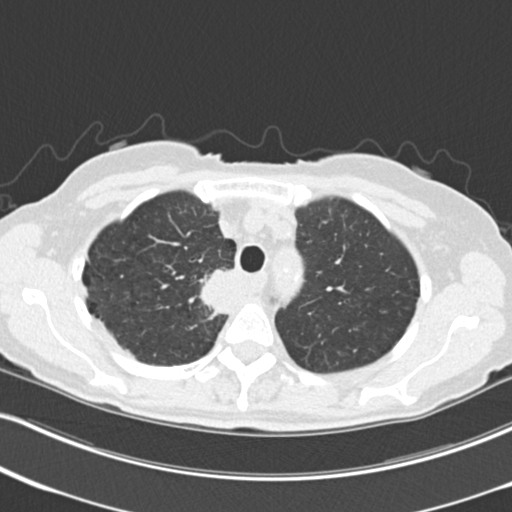
Low-dose screening chest CT, one axial slice. Slice 177 of 226 in the series (ordered by position). 120 kVp. Lung window (W 1500 / L -600 HU). 2 mm slice thickness. 512 × 512 image matrix, field of view 322 × 322 mm.
Outlined on this slice (manually delineated by an expert):
- lesion 1 (tumor, mediastinum): bounding box (x1, y1, x2, y2) in pixels: (200, 269, 234, 314)